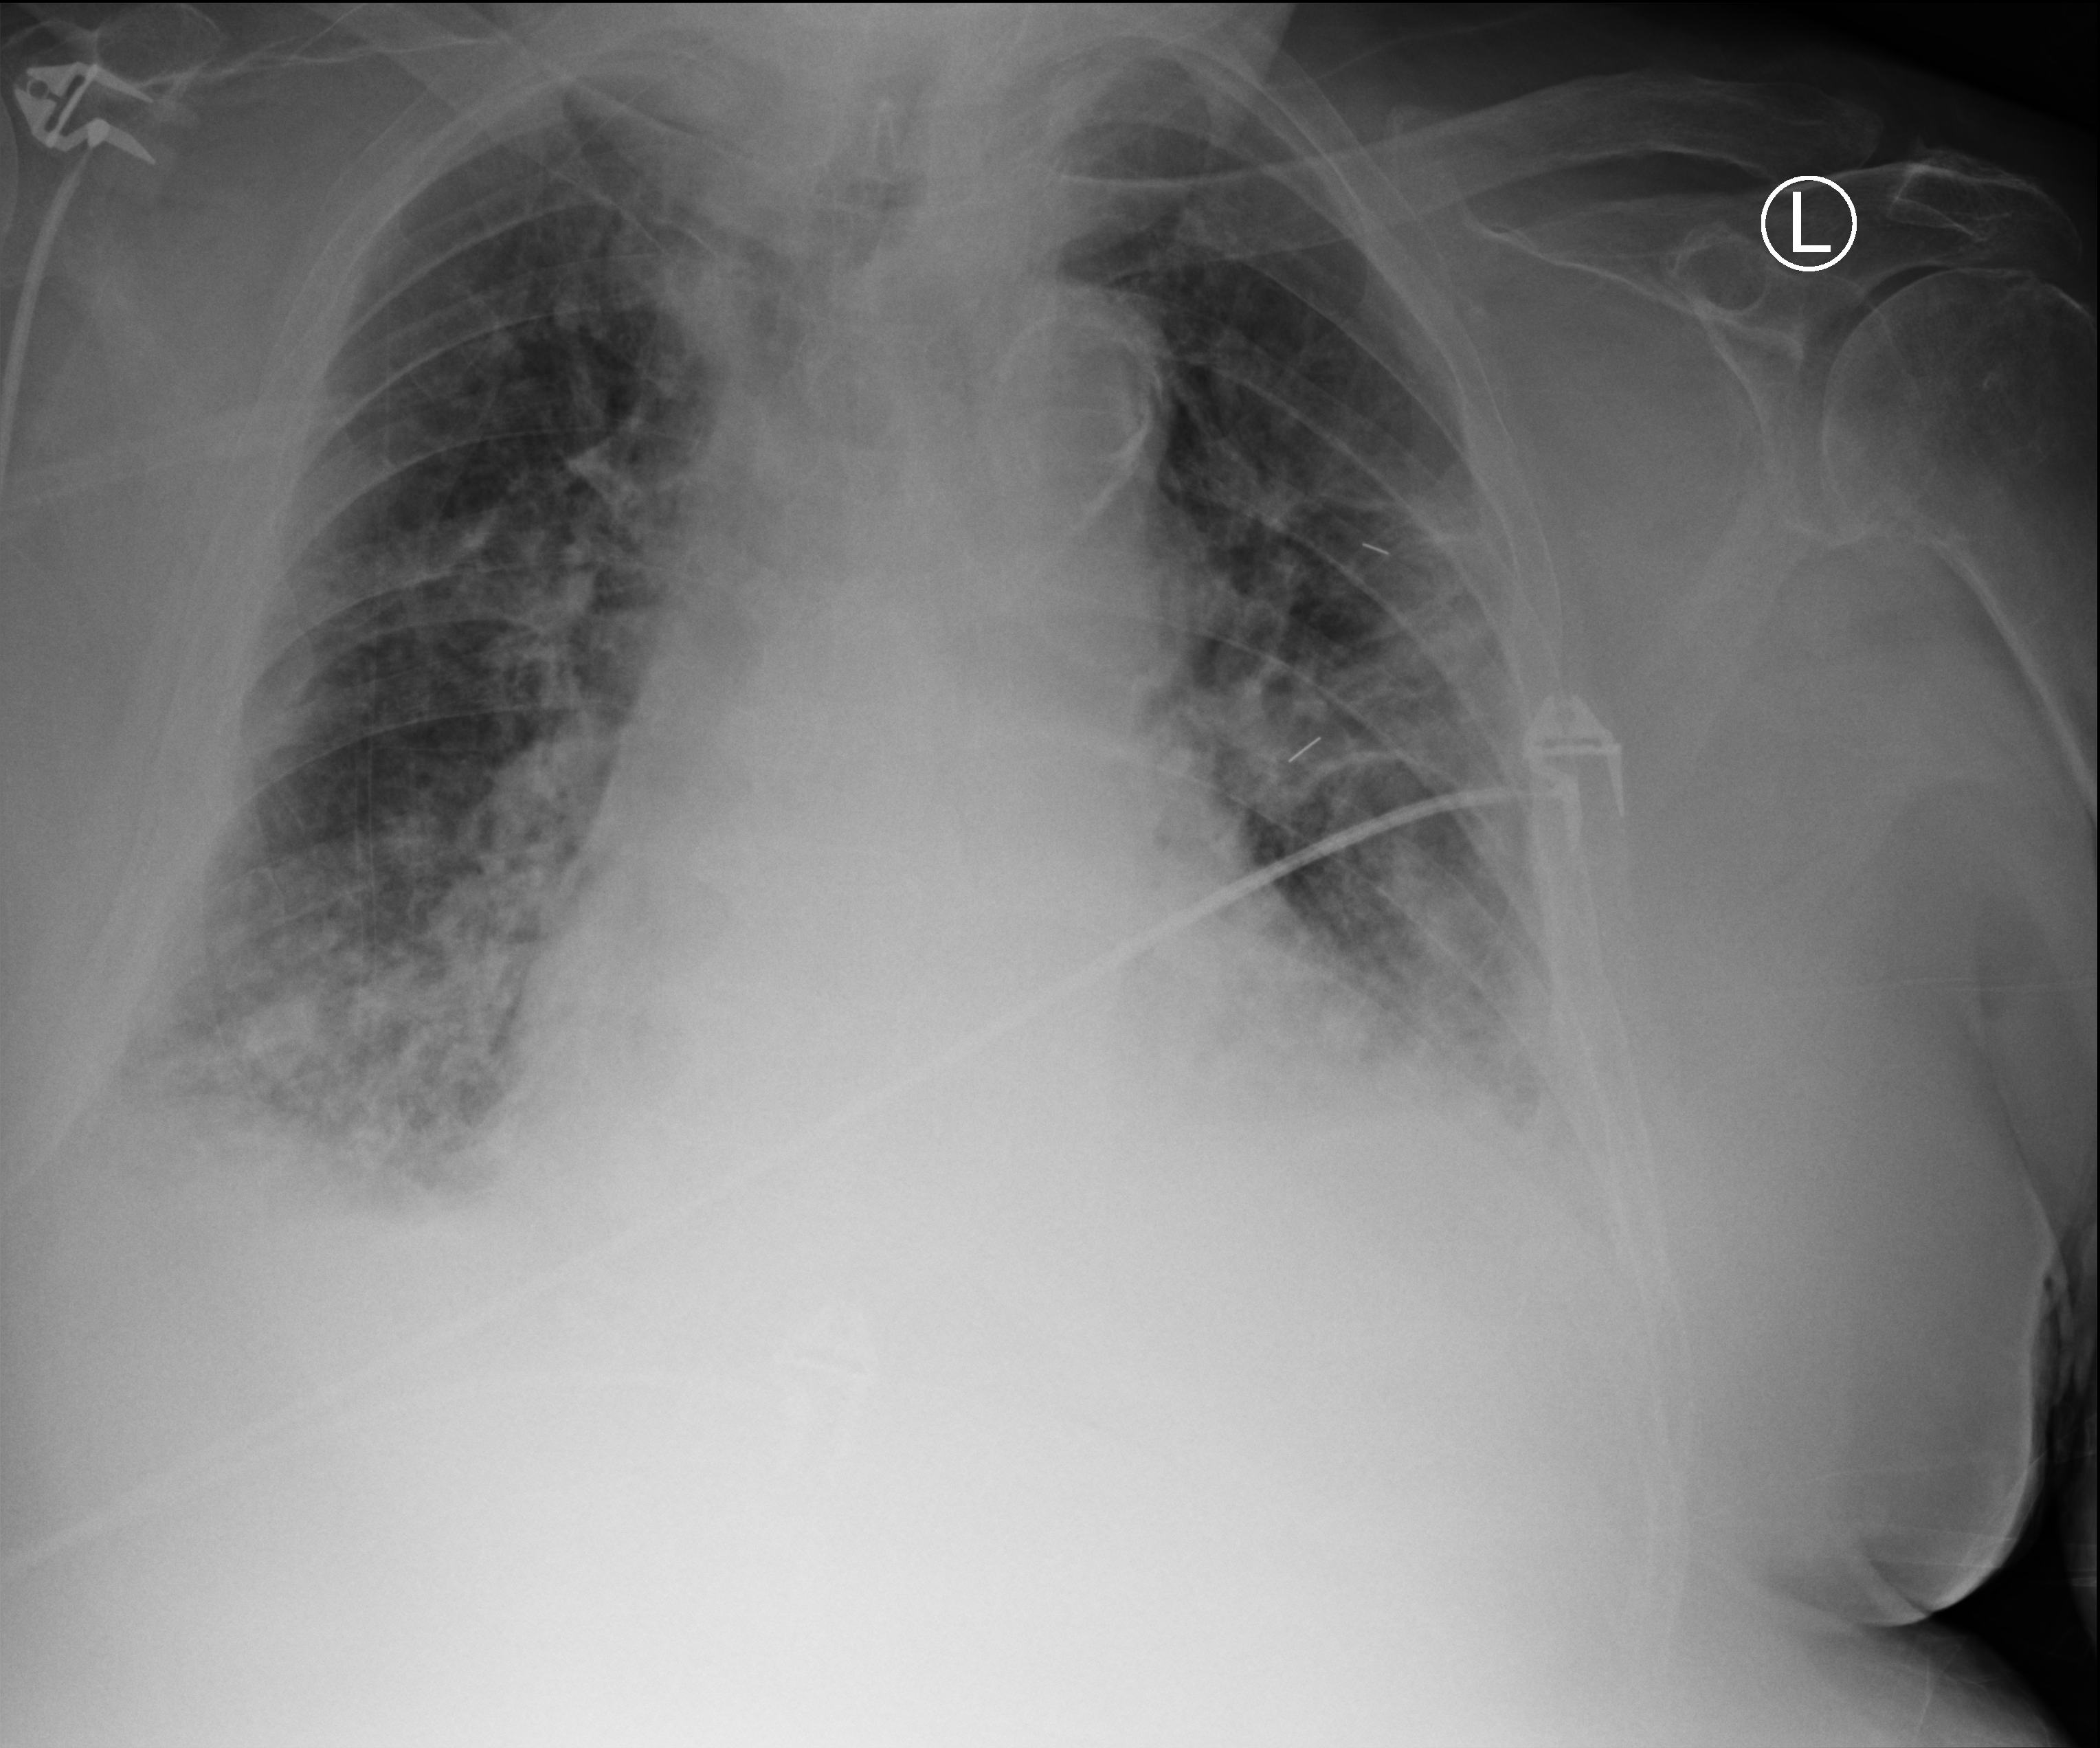
Chest X-ray (portable), anteroposterior (AP) projection. Patient hospitalised with COVID-19; male, aged 75–90 years.
Admission-level facts for this patient (not findings on this image; timing relative to this image not recorded):
- length of hospital stay: 14 days
- admitted to intensive care during this hospital stay: no
- mechanically ventilated during this hospital stay: no